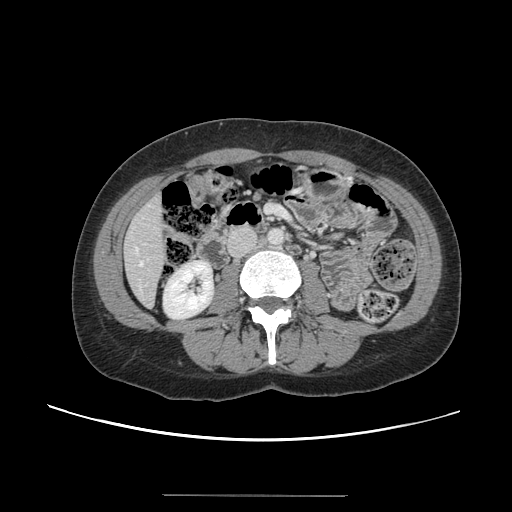
Contrast-enhanced abdominal CT, one axial slice. Position 36 of 144 along the scan axis. 120 kVp. Intravenous contrast given. Soft-tissue window (W 400 / L 40 HU). 2.5 mm slice thickness. 512 × 512 image matrix. Female patient, age 53 years. Case-level facts recorded for this patient, not image findings: diagnosis: colorectal cancer liver metastases, imaged before liver resection; multiple liver metastases: yes; largest metastasis: 1.1 cm; disease in both lobes: no.
Annotated regions visible in this slice (manually delineated by an expert):
- hepatic veins: bounding box [x1, y1, x2, y2] px = [136, 249, 143, 266]
- liver: [124, 196, 167, 306]
- planned liver remnant (the part of the liver to remain after resection): [125, 194, 166, 306]